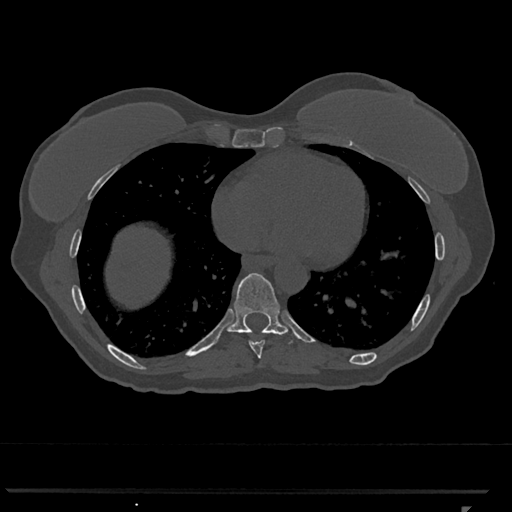
CT including the spine, one axial slice; position 635 of 793 along the scan axis; reconstruction kernel Br40s/3; bone window (W 1800 / L 400 HU); 512 × 512 image matrix. Female patient, age 62 years. Case-level facts recorded for this patient, not image findings: primary cancer: renal.
Outlined on this slice (semi-automatically segmented with operator editing):
- T8 vertebra: box from (x=249, y=340) to (x=265, y=359) px
- T9 vertebra: (x=227, y=273)–(x=297, y=344)